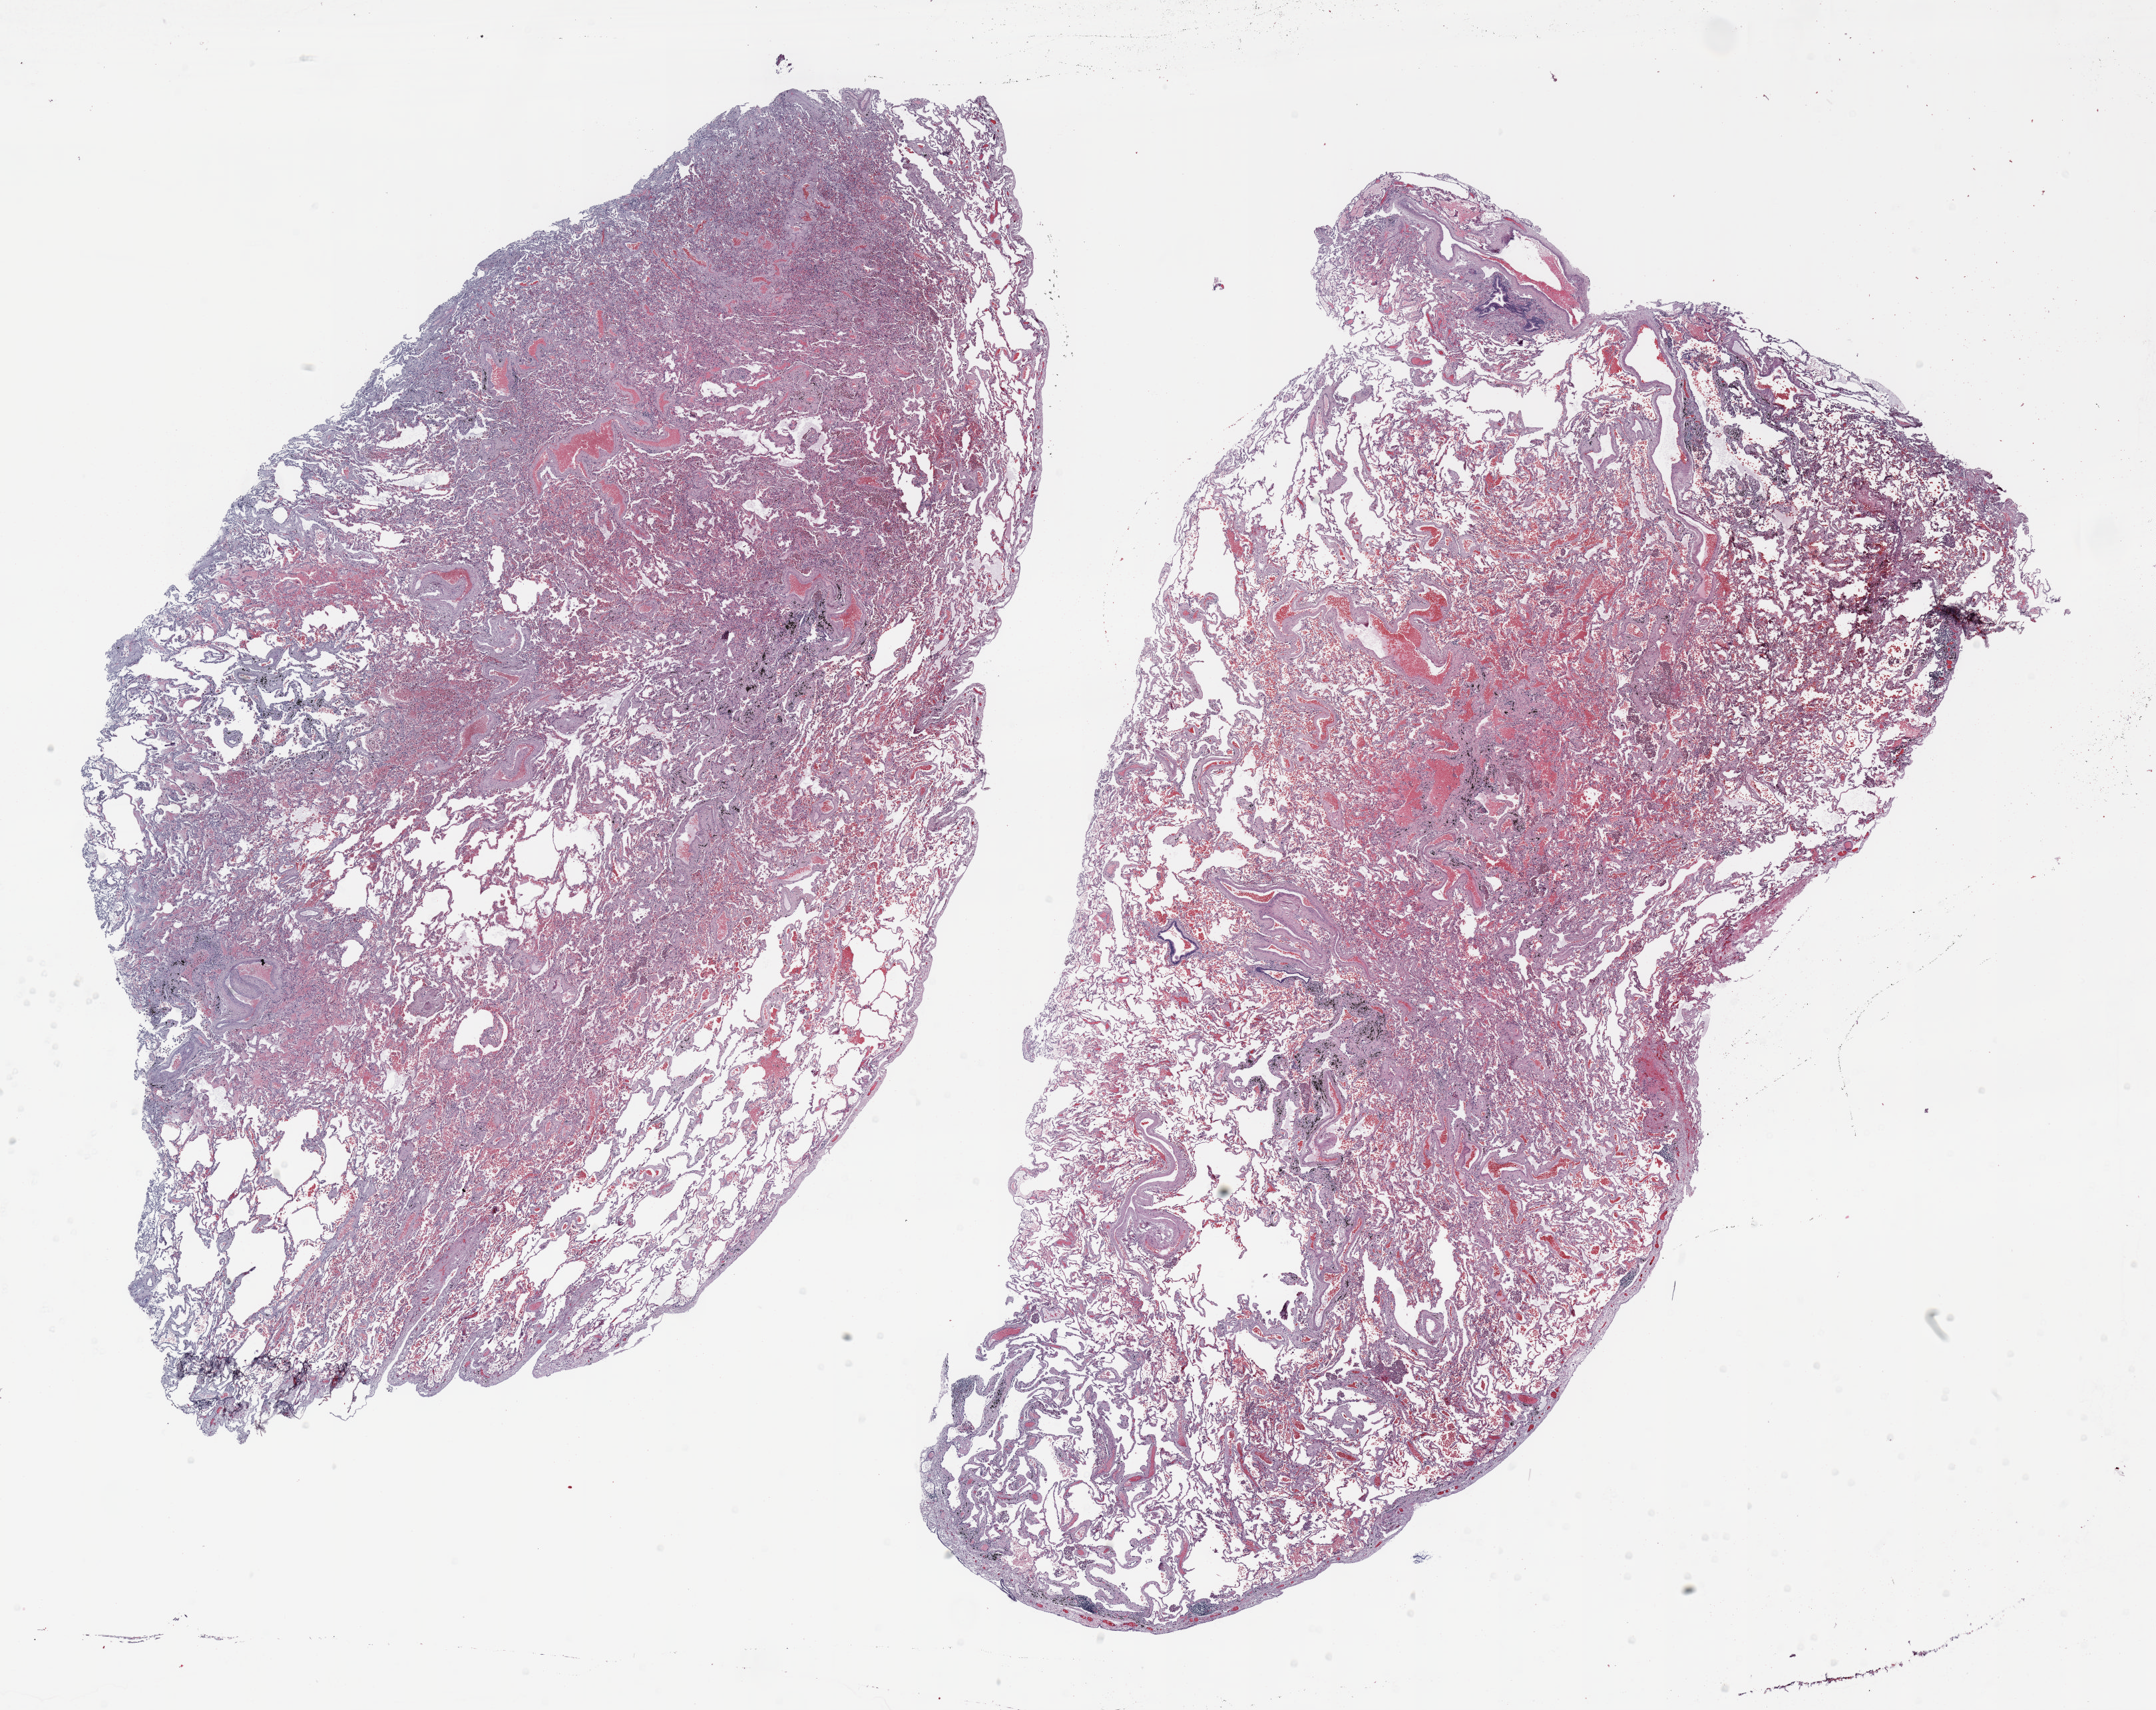
Whole-slide histology image, Hematoxylin and eosin (H&E) stained, whole scanned area (about 26.0 x 20.6 mm, acquisition: 20x scan) shown as a low-resolution overview. Formalin-fixed paraffin-embedded (FFPE) section. Lung. Male, age 73 at enrolment. Current smoker at enrolment. Grade: well differentiated (G1).
Primary tumour location (clinical record): right middle lobe. Tumour size (pathology): 11 mm. Stage (AJCC 6th edition): IA. Participant's lung-cancer diagnosis: Bronchiolo-alveolar adenocarcinoma, NOS (ICD-O-3 8250/3).